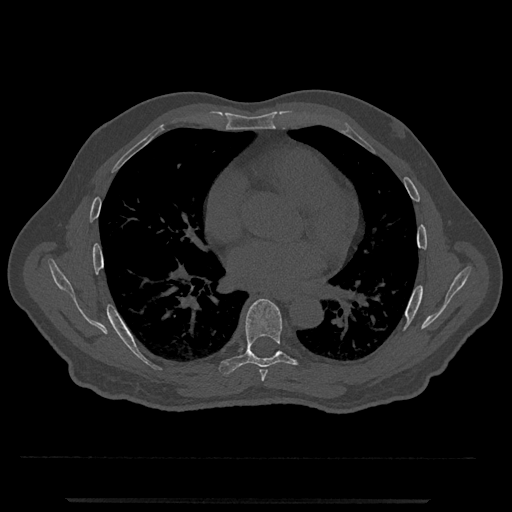
CT including the spine, one axial slice; position 689 of 797 along the scan axis; reconstruction kernel Br40s/3; 120 kVp; bone window (W 1800 / L 400 HU); 0.5 mm slice thickness; 512 × 512 image matrix. Patient: male, 63 years. From the clinical record (not read from this slice): primary cancer: prostate.
Structures marked on this image (semi-automatically segmented with operator editing):
- T6 vertebra: bounding box (x1, y1, x2, y2) in pixels: (259, 370, 268, 382)
- T7 vertebra: (219, 299, 302, 375)